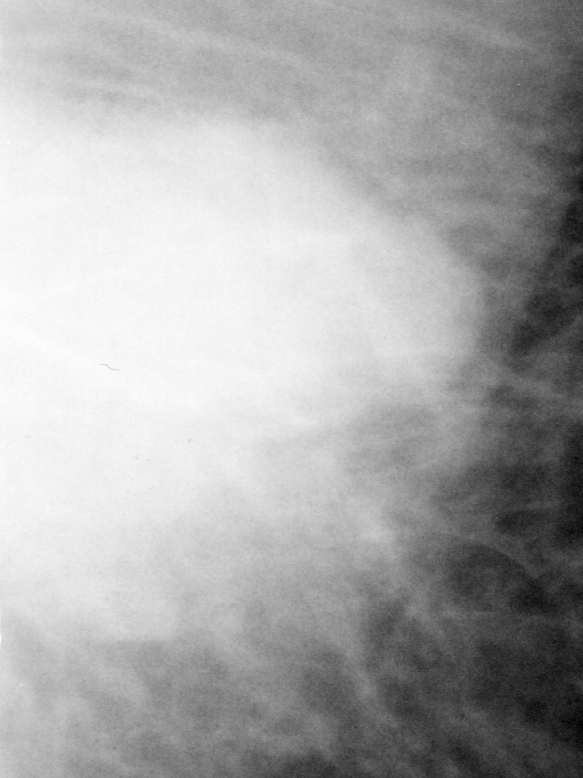
Cropped region of a digitized screen-film mammogram centred on a radiologist-marked abnormality; left breast; MLO view.
Mass, shape lobulated, margins microlobulated; BI-RADS assessment category 5; subtlety rating 5 on a 1 (subtle) to 5 (obvious) scale; pathology result (as recorded, not read from the image): malignant.